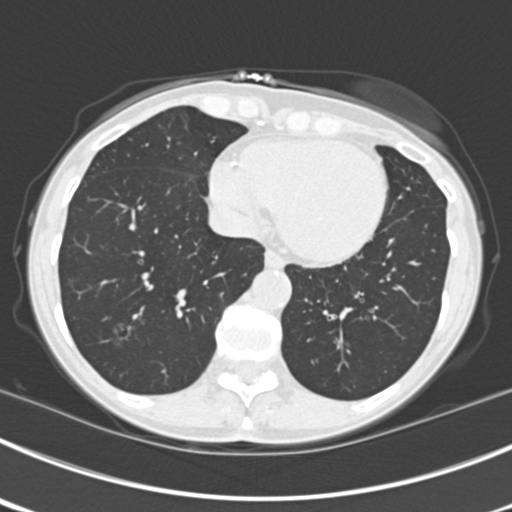
Chest CT (low-dose screening protocol), one axial image. Third screening round (two years after baseline). Lung window (W 1500 / L -600 HU). Slice 145 of 225 in the series. Female participant, aged 63 years at enrolment. Current smoker at enrolment.
• Lesion marked by an expert reader, box from (x=103, y=310) to (x=148, y=357) px.
• The screening reader recorded 9 non-calcified nodules or masses ≥4 mm on this exam (left upper lobe, right upper lobe, left upper lobe, left lower lobe, right middle lobe, left lower lobe, left lower lobe, right lower lobe, right lower lobe); which of them this box marks is not recorded.
• Official screen result: positive, other.
• Participant outcome: lung cancer diagnosed 15 days after this screen — bronchiolo-alveolar adenocarcinoma, NOS, right upper lobe, right middle lobe, right lower lobe, left upper lobe, left lower lobe, moderately differentiated (G2), stage IV (AJCC 6th edition).